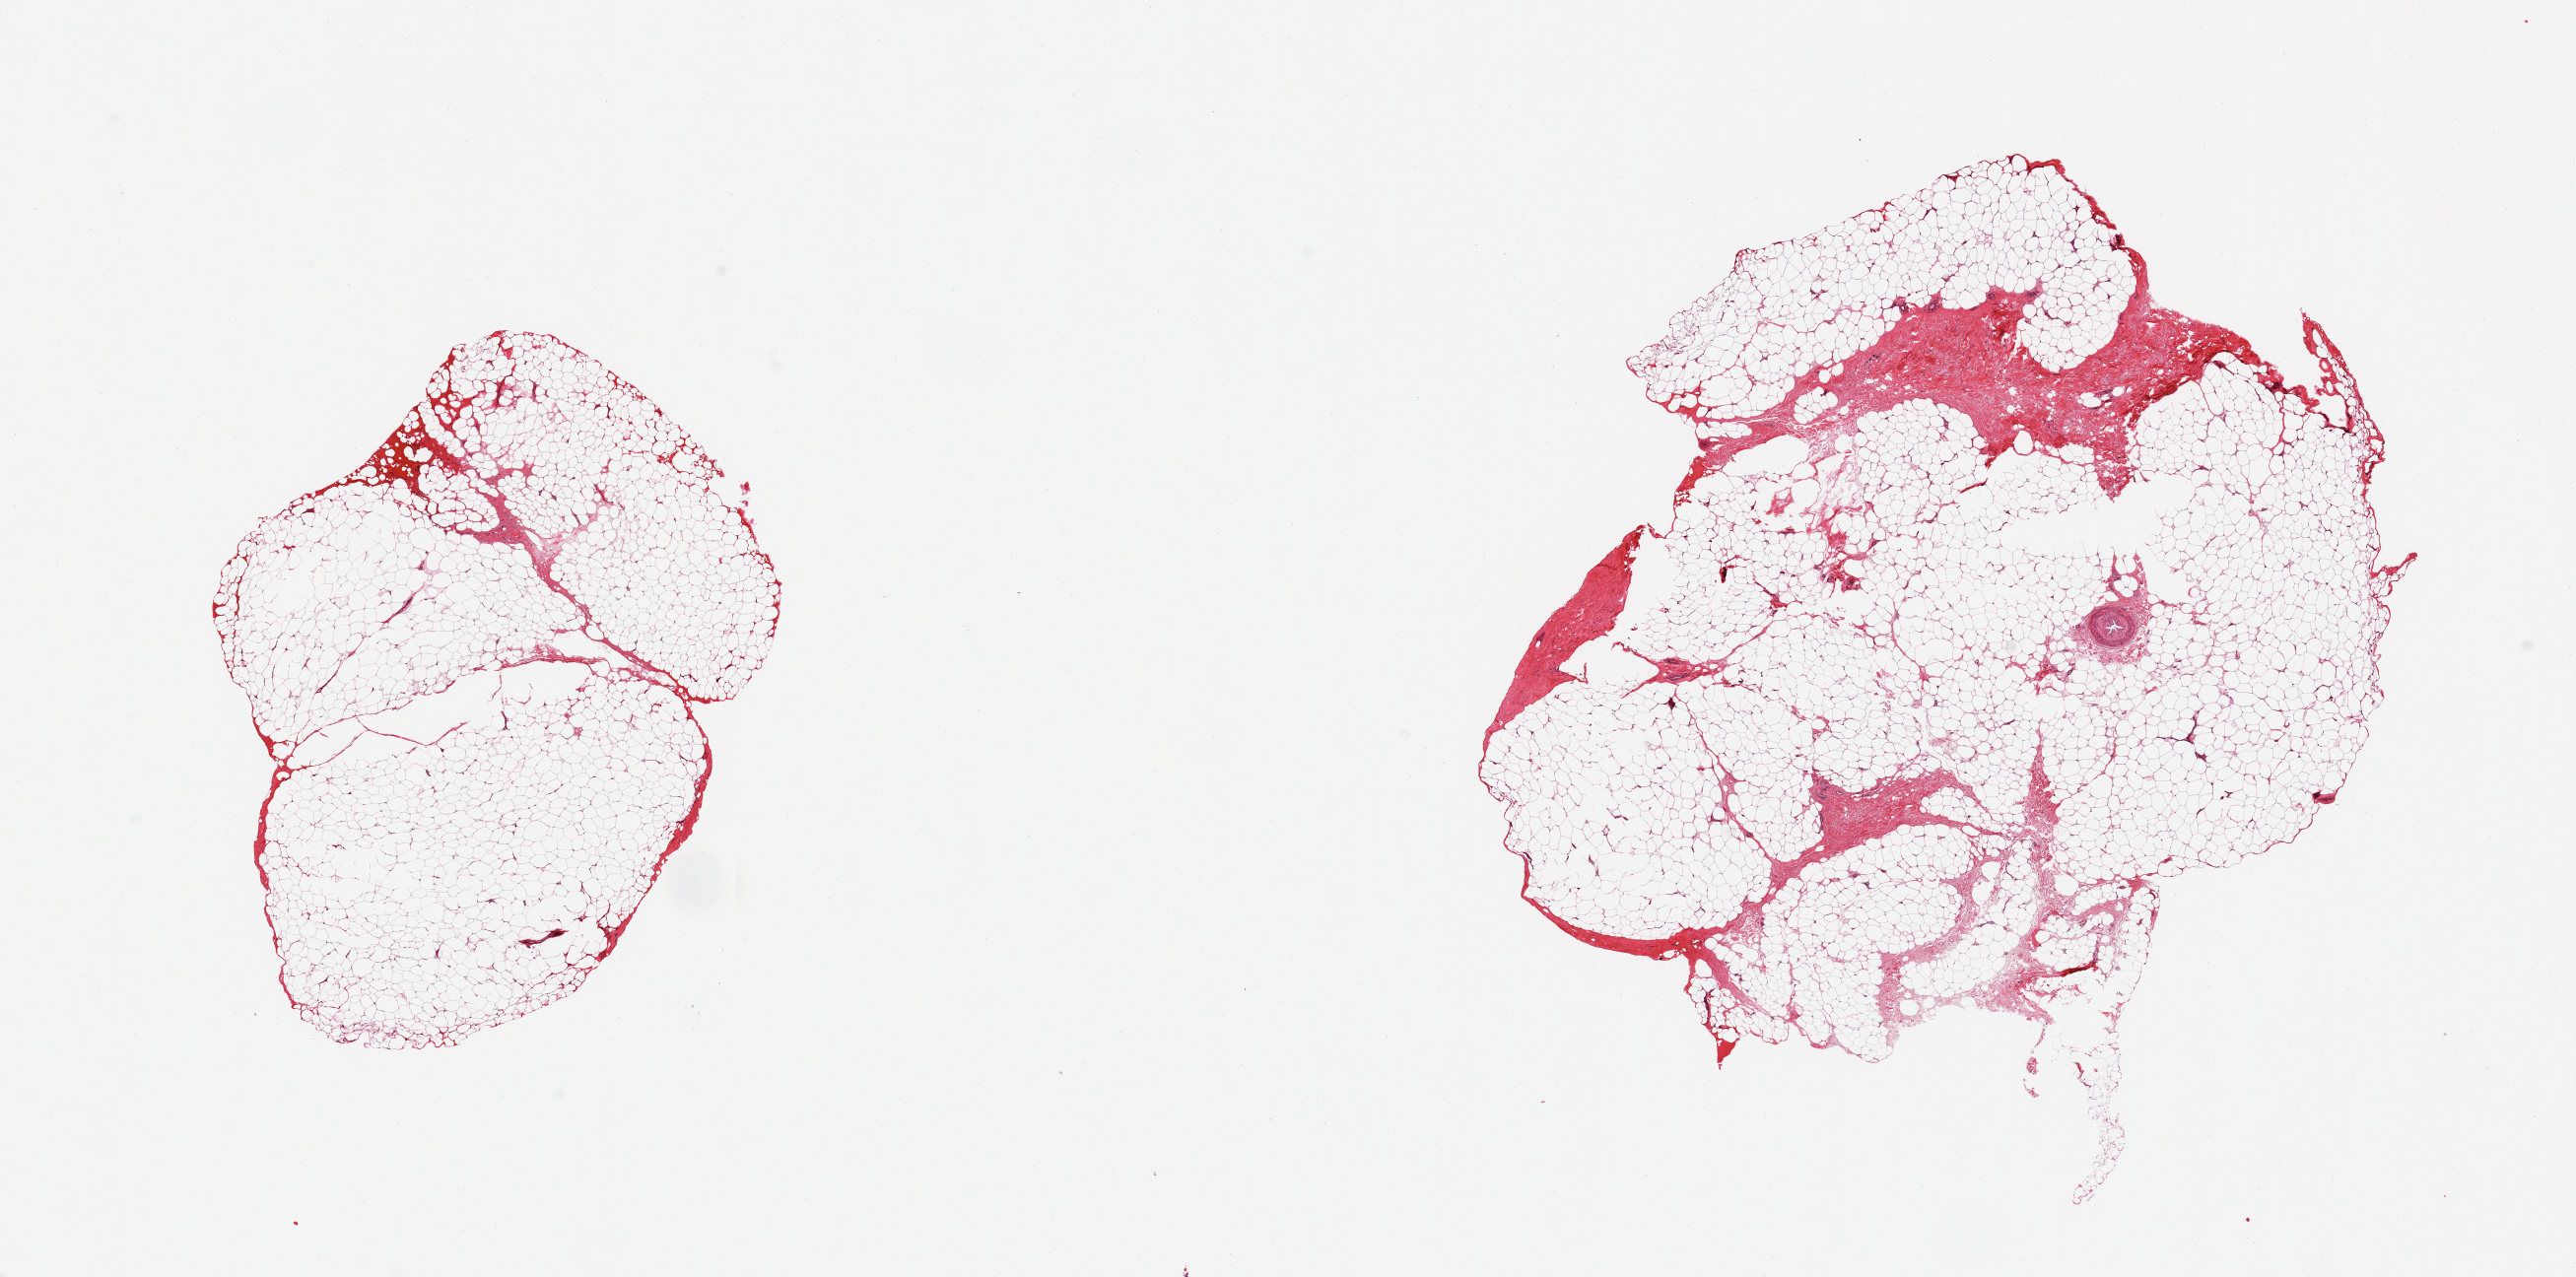
Digitized H&E-stained section, brightfield — low-resolution overview of the scanned area, about 20.7 x 10.2 mm (slide scanned at 20x); PAXgene-fixed paraffin-embedded (PFPE) section; target tissue: adipose tissue; tissue donor sample. Donor: male.
Reviewer comment on this tissue sample: 2 pieces; mature adipose tissue and 5% and 15% fibrovascular component.